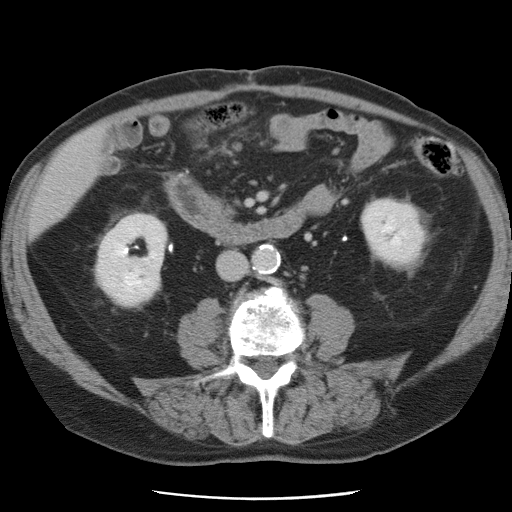
Contrast-enhanced abdominal CT, one axial slice; position 16 of 78 along the scan axis; 120 kVp; intravenous contrast given; soft-tissue window (W 400 / L 40 HU); 512 × 512 image matrix. Male patient, age 75 years. From the clinical record (not read from this slice): diagnosis: colorectal cancer liver metastases, imaged before liver resection; multiple liver metastases: yes; largest metastasis: 2.4 cm.
Structures marked on this image (expert manual segmentation):
- liver: box from (x=33, y=132) to (x=104, y=231) px
- planned liver remnant (the part of the liver to remain after resection): (x=32, y=131)–(x=104, y=232)